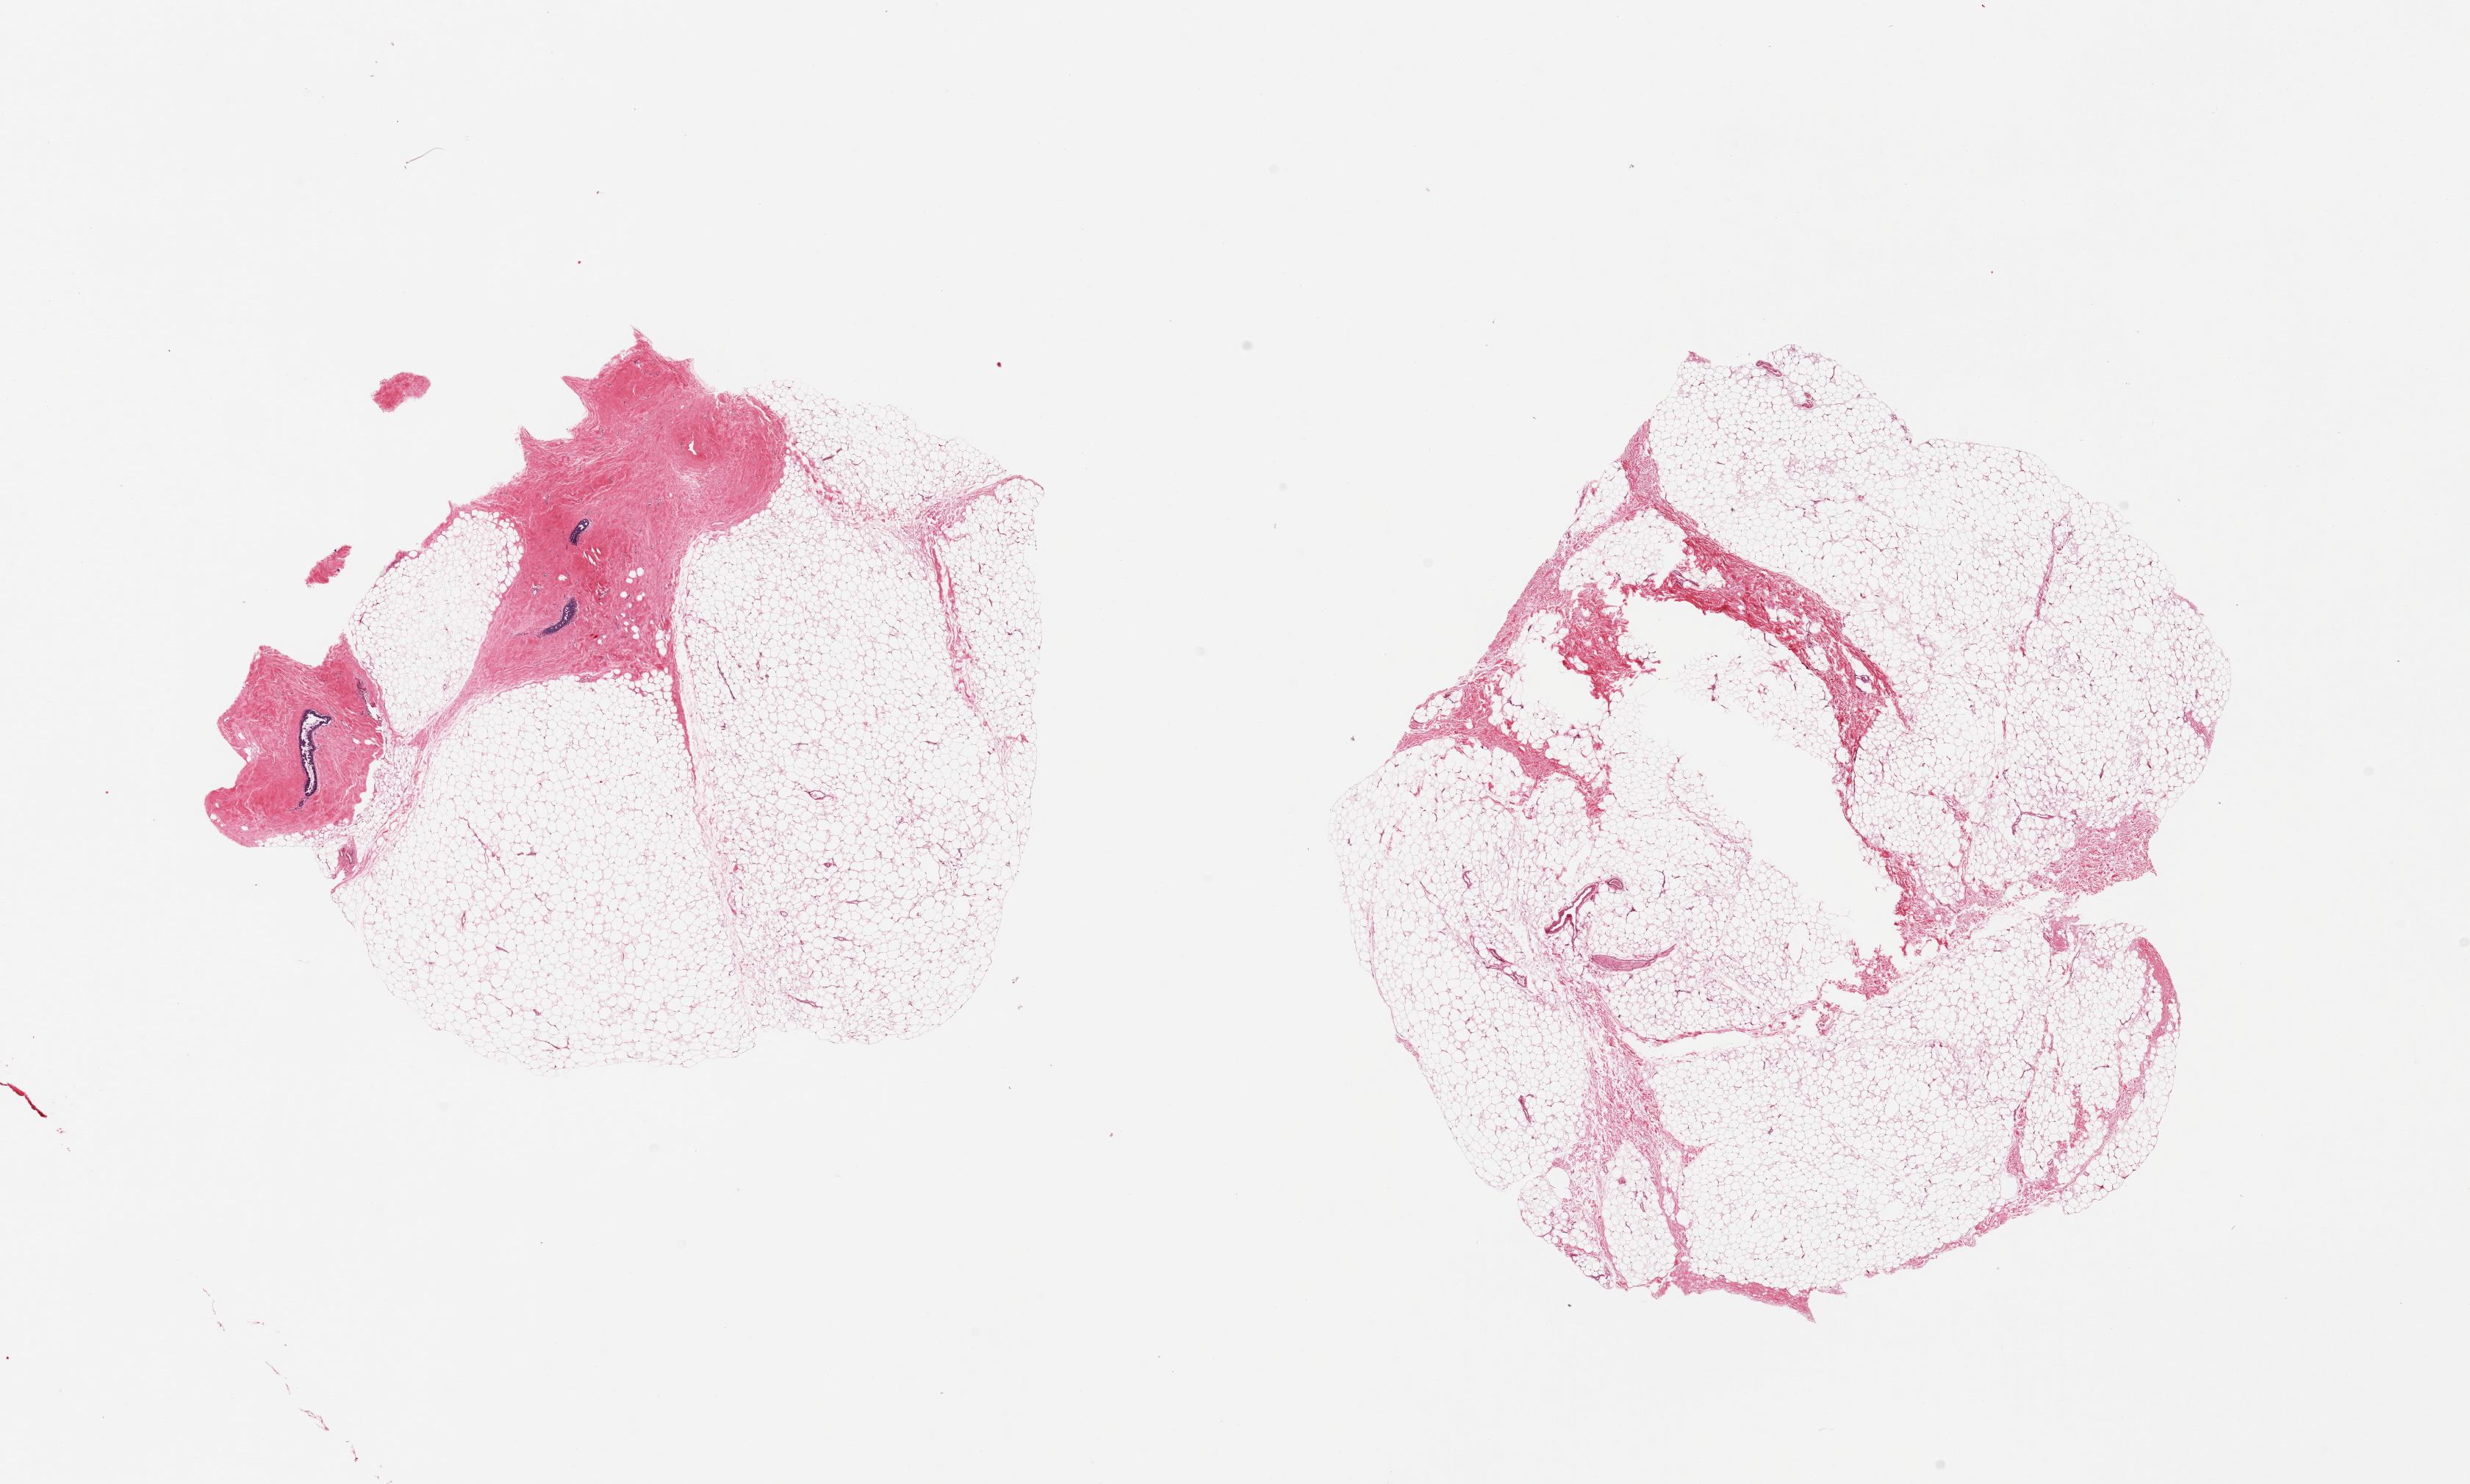
Digitized hematoxylin and eosin (H&E)-stained section, shown as a low-resolution overview of the whole scanned area (about 26.6 x 16.0 mm, acquisition: 20x scan), PAXgene-fixed paraffin-embedded (PFPE) section, target tissue: breast, tissue donor sample. Donor: male.
* pathologist's review note for this sample: 2 pieces, one with prominent focal gynecomastoid stromal and ductal hyperplasia; duct elements